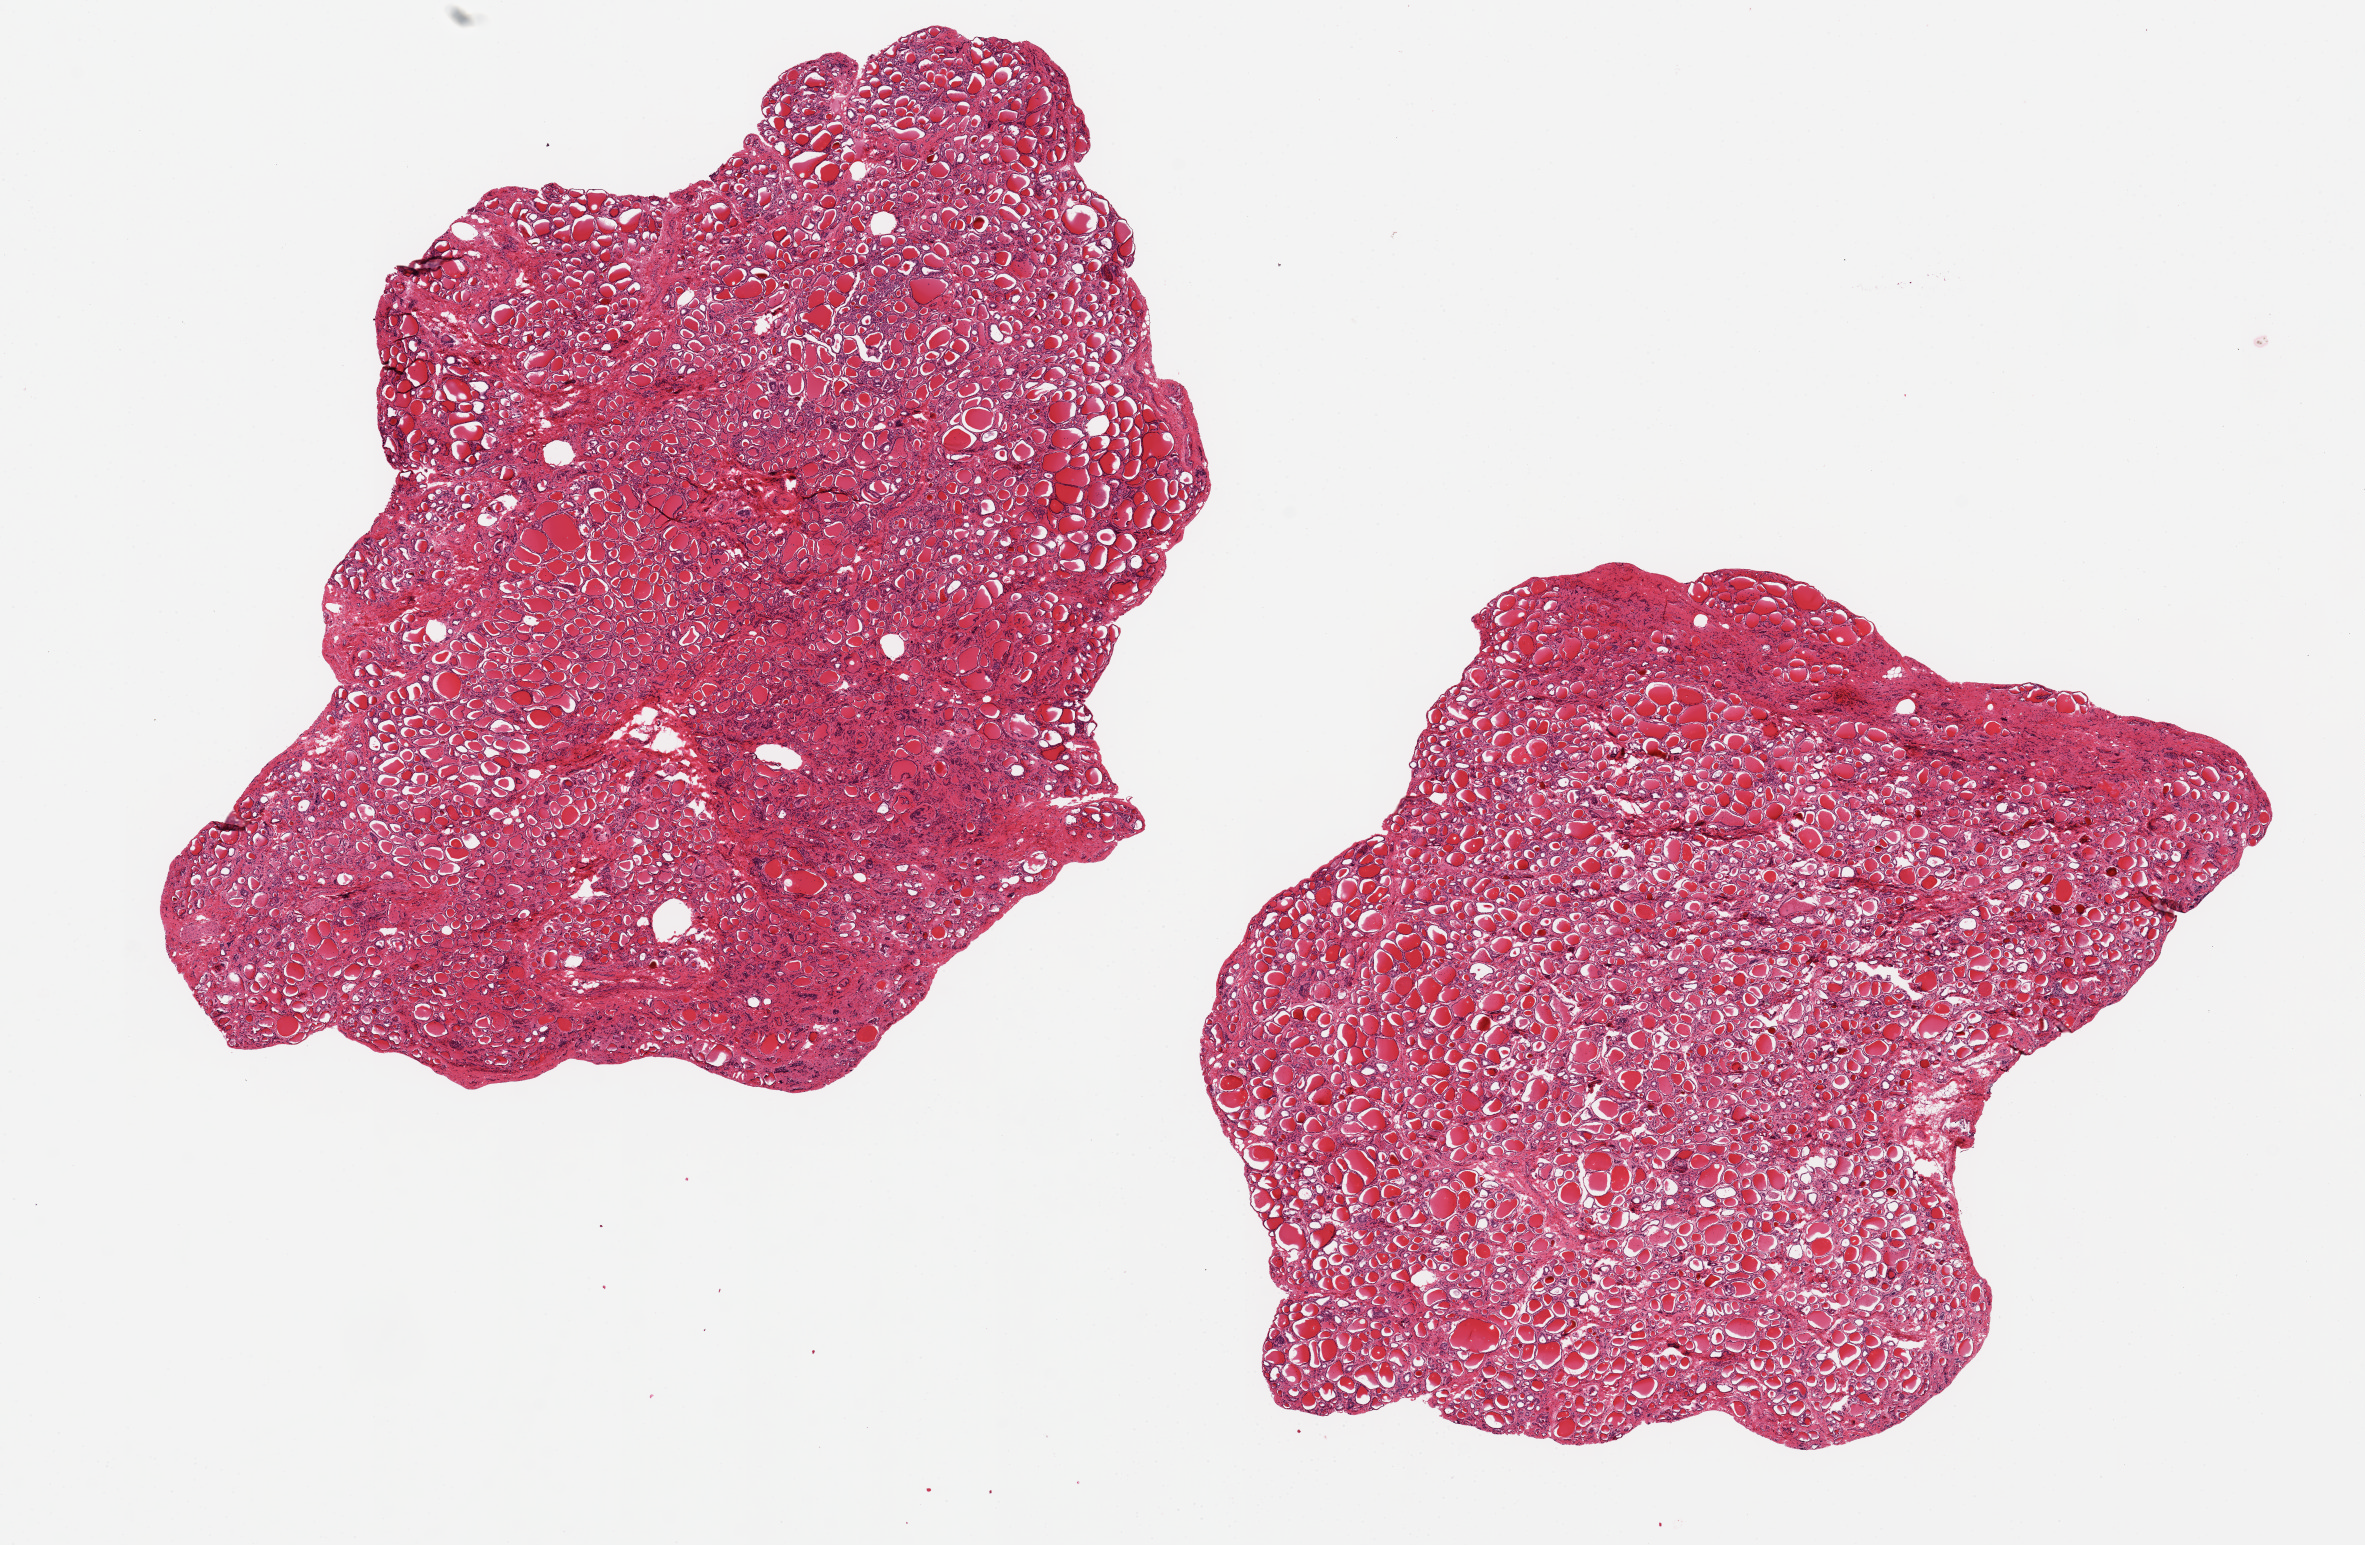
Whole-slide image, H&E stain, a low-resolution overview of the entire scanned area, about 18.7 x 12.2 mm (from a 20x scan). PAXgene-fixed paraffin-embedded (PFPE) section. Target tissue: thyroid. Donor tissue sample. Donor: male.
- reviewer comment on this tissue sample: 2 pieces 10x7&8x5 mm; no nodularity; focal fibrosis